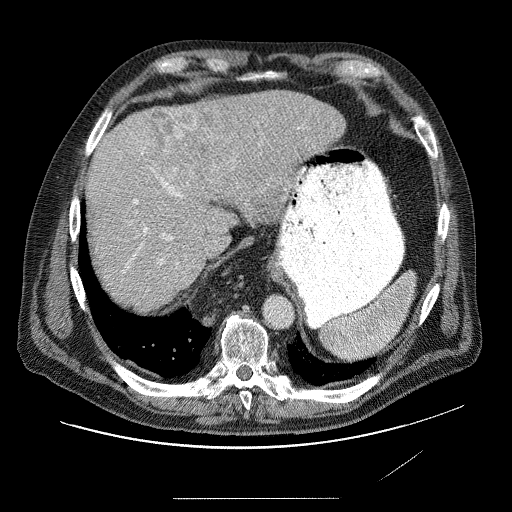
Contrast-enhanced abdominal CT (liver protocol), one axial slice. Slice 62 of 89 in the series (ordered by position). Reconstruction kernel STANDARD. 120 kVp. Soft-tissue window (W 400 / L 40 HU). 2.5 mm slice thickness. 512 × 512 image matrix. Case-level facts recorded for this patient, not image findings: diagnosis: hepatocellular carcinoma (patient treated with transarterial chemoembolisation; whether this scan precedes or follows treatment is not stated here); TNM stage (as recorded): Stage-IVA.
Structures marked on this image (semi-automatically segmented with operator editing):
- liver parenchyma outside the tumour (the mass and vessels are separate outlines, so this box may not span the whole liver): bounding box (x1, y1, x2, y2) in pixels: (86, 90, 346, 296)
- mass: (128, 103, 280, 221)
- liver vessels: (100, 138, 279, 274)